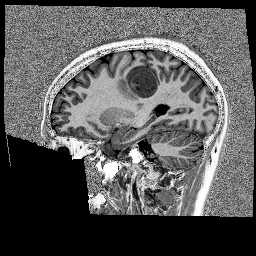
Brain MRI from a brain-tumour surgery series, one sagittal slice. Slice 65 of 176 in the series (ordered by position). 1 mm slice thickness. 256 × 256 image matrix, field of view 256 × 256 mm. Case-level facts recorded for this patient, not image findings: histopathology: Glioblastoma; WHO grade: 4; IDH mutation: no.
Annotated regions visible in this slice (expert manual segmentation):
- tumour: bounding box <118,60,175,94> (left, top, right, bottom; pixels)